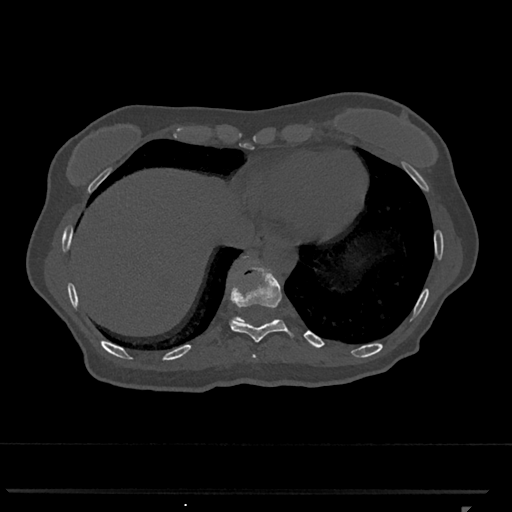
CT including the spine, one axial slice; position 563 of 793 along the scan axis; bone window (W 1800 / L 400 HU); 0.5 mm slice thickness; 512 × 512 image matrix. Patient: female, 62 years. From the clinical record (not read from this slice): primary cancer: renal.
Outlined on this slice (semi-automatically segmented with operator editing):
- T10 vertebra: bounding box (x1, y1, x2, y2) in pixels: (229, 263, 294, 343)
- T11 vertebra: (232, 256, 275, 322)
- T9 vertebra: (252, 355, 256, 358)